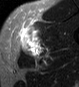
MRI of an extremity soft-tissue mass, one axial slice. STIR. MR volume resampled by the dataset authors to the PET/CT grid (not the native acquisition matrix). 3.27 mm slice thickness. 79 × 87 image matrix, field of view 77 × 85 mm. Male patient. Case-level facts recorded for this patient, not image findings: histological type: pleiomorphic leiomyosarcoma; grade: high; site of the primary tumour: left thigh.
Outlined on this slice (expert contour drawn on MRI and transferred to this co-registered scan by the dataset authors):
- gross tumour volume including surrounding oedema: bounding box [x1, y1, x2, y2] px = [20, 25, 44, 58]
- gross tumour volume (mass): [27, 43, 37, 54]